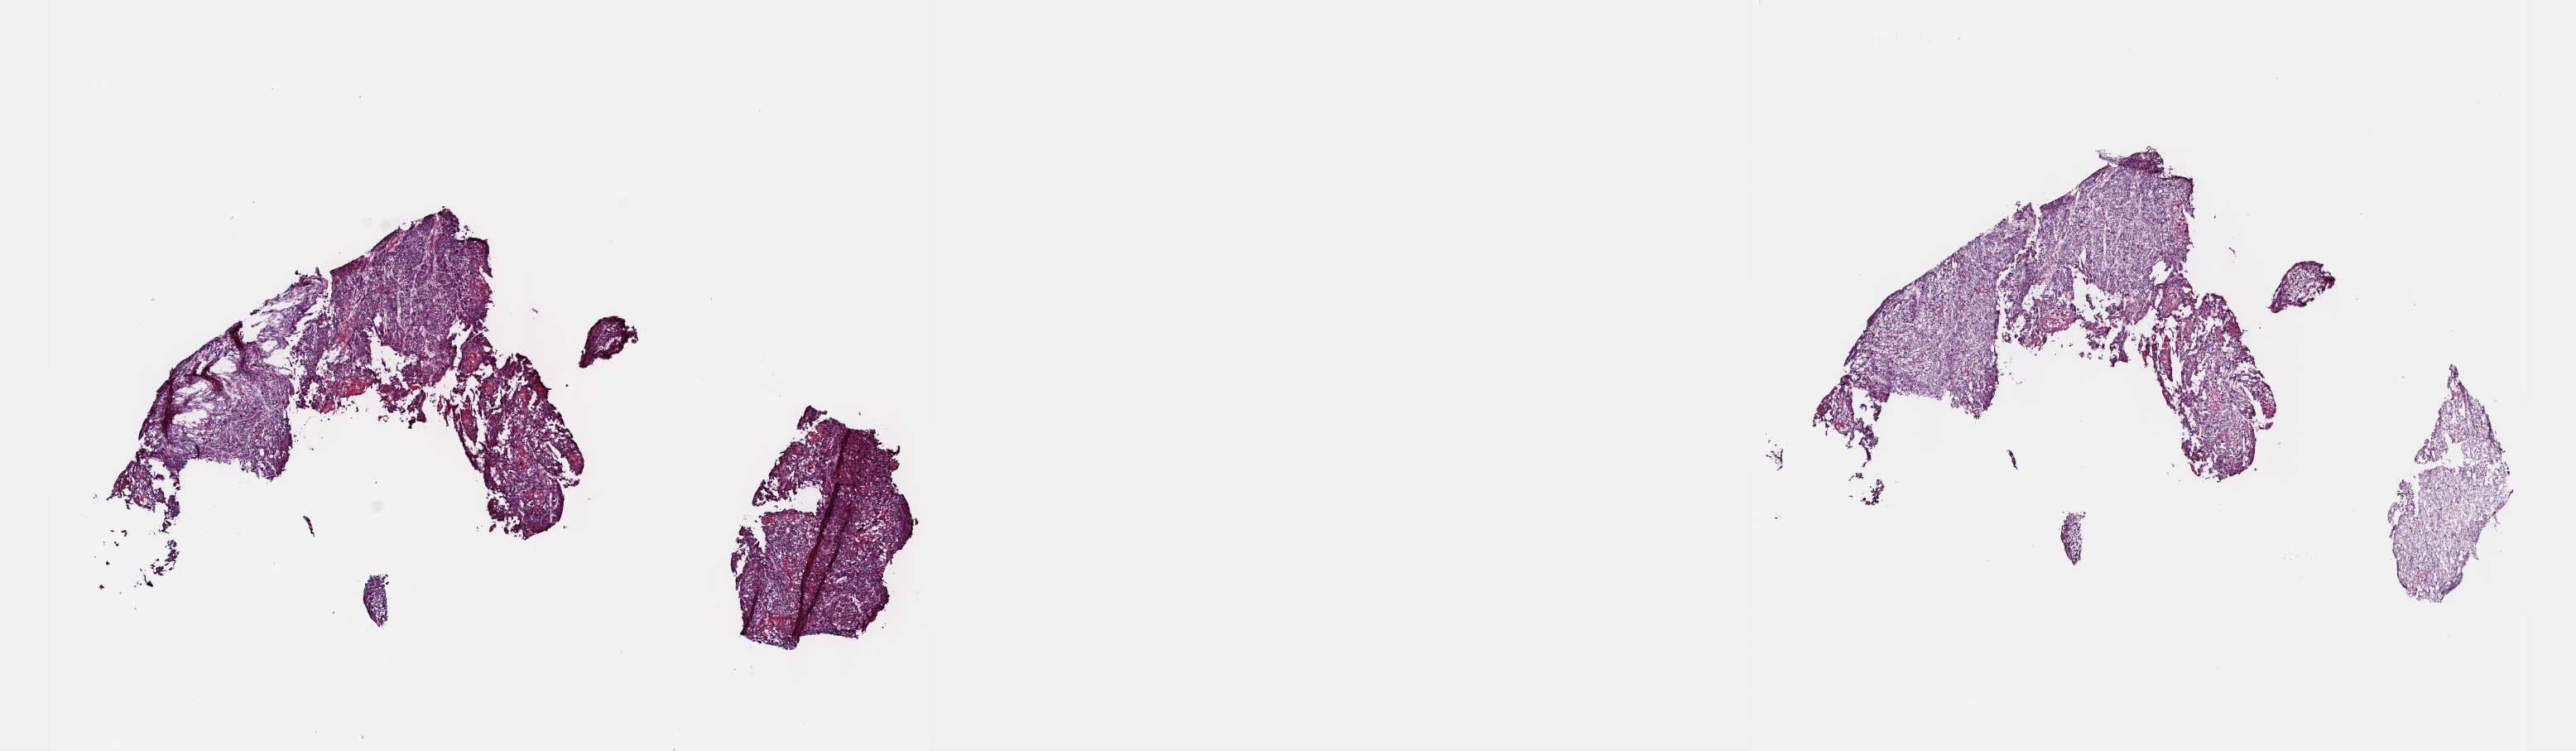
Whole-slide histology image, H&E-stained, low-resolution overview of the scanned area, about 25.1 x 7.3 mm (acquisition: 40x scan). Frozen section from the top of the tissue portion. Sample: primary tumour, cervix. Female, age 72 years at initial diagnosis. Histologic grade: G3 (poorly differentiated). Slide review estimates, as recorded: tumour cells 80%, tumour nuclei 80%, normal cells 0%, stromal cells 20%, necrosis 0%. Inflammatory infiltration, as recorded: lymphocyte infiltration 5%, monocyte infiltration 3%, neutrophil infiltration 2%.
Histologic diagnosis: Squamous cell carcinoma, keratinizing, NOS (cervix uteri). FIGO stage: IVB.